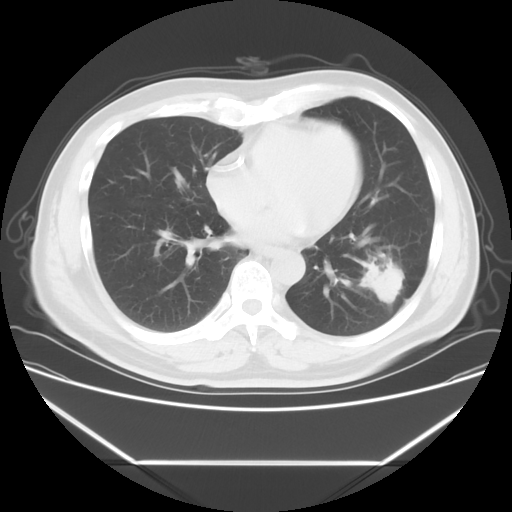
Chest CT, one axial slice. Slice 24 of 57 in the series (ordered by position). Reconstruction kernel STANDARD. Lung window (W 1500 / L -600 HU). 5 mm slice thickness. 512 × 512 image matrix, field of view 384 × 384 mm. Male patient, age 53 years. Case-level facts recorded for this patient, not image findings: clinical TNM (as recorded): T1c N0 M0.
Annotated regions visible in this slice (bounding box drawn by a radiologist):
- lung tumour (recorded histology: adenocarcinoma): bounding box (x1, y1, x2, y2) in pixels: (354, 244, 410, 311)